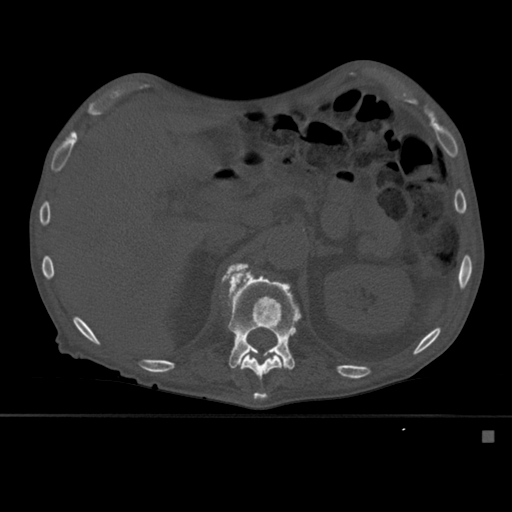
CT including the spine, one axial slice; slice 265 of 527 in the series (ordered by position); bone window (W 1800 / L 400 HU); 1.5 mm slice thickness; 512 × 512 image matrix. Male patient, age 78 years. Case-level facts recorded for this patient, not image findings: primary cancer: prostate.
Outlined on this slice (semi-automatic segmentation, software-assisted and operator-edited):
- L1 vertebra: bounding box (x1, y1, x2, y2) in pixels: (221, 273, 301, 400)
- T12 vertebra: (226, 262, 282, 399)